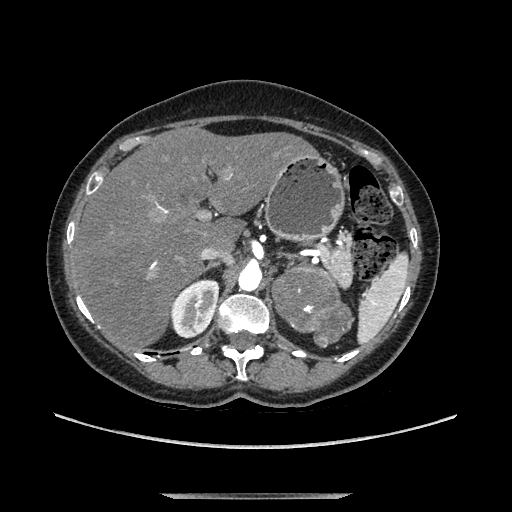
Contrast-enhanced abdominal CT, one axial slice. Soft-tissue window (W 400 / L 40 HU). 1.25 mm slice thickness. 512 × 512 image matrix. Female patient. From the clinical record (not read from this slice): diagnosis: adrenocortical carcinoma; tumour side: left adrenal; tumour size at pathology: 9 cm; Ki-67 index: 2 %; stage (as recorded): 3.
Annotated regions visible in this slice (semi-automatically segmented with operator editing):
- mass: bounding box <275,266,348,344> (left, top, right, bottom; pixels)